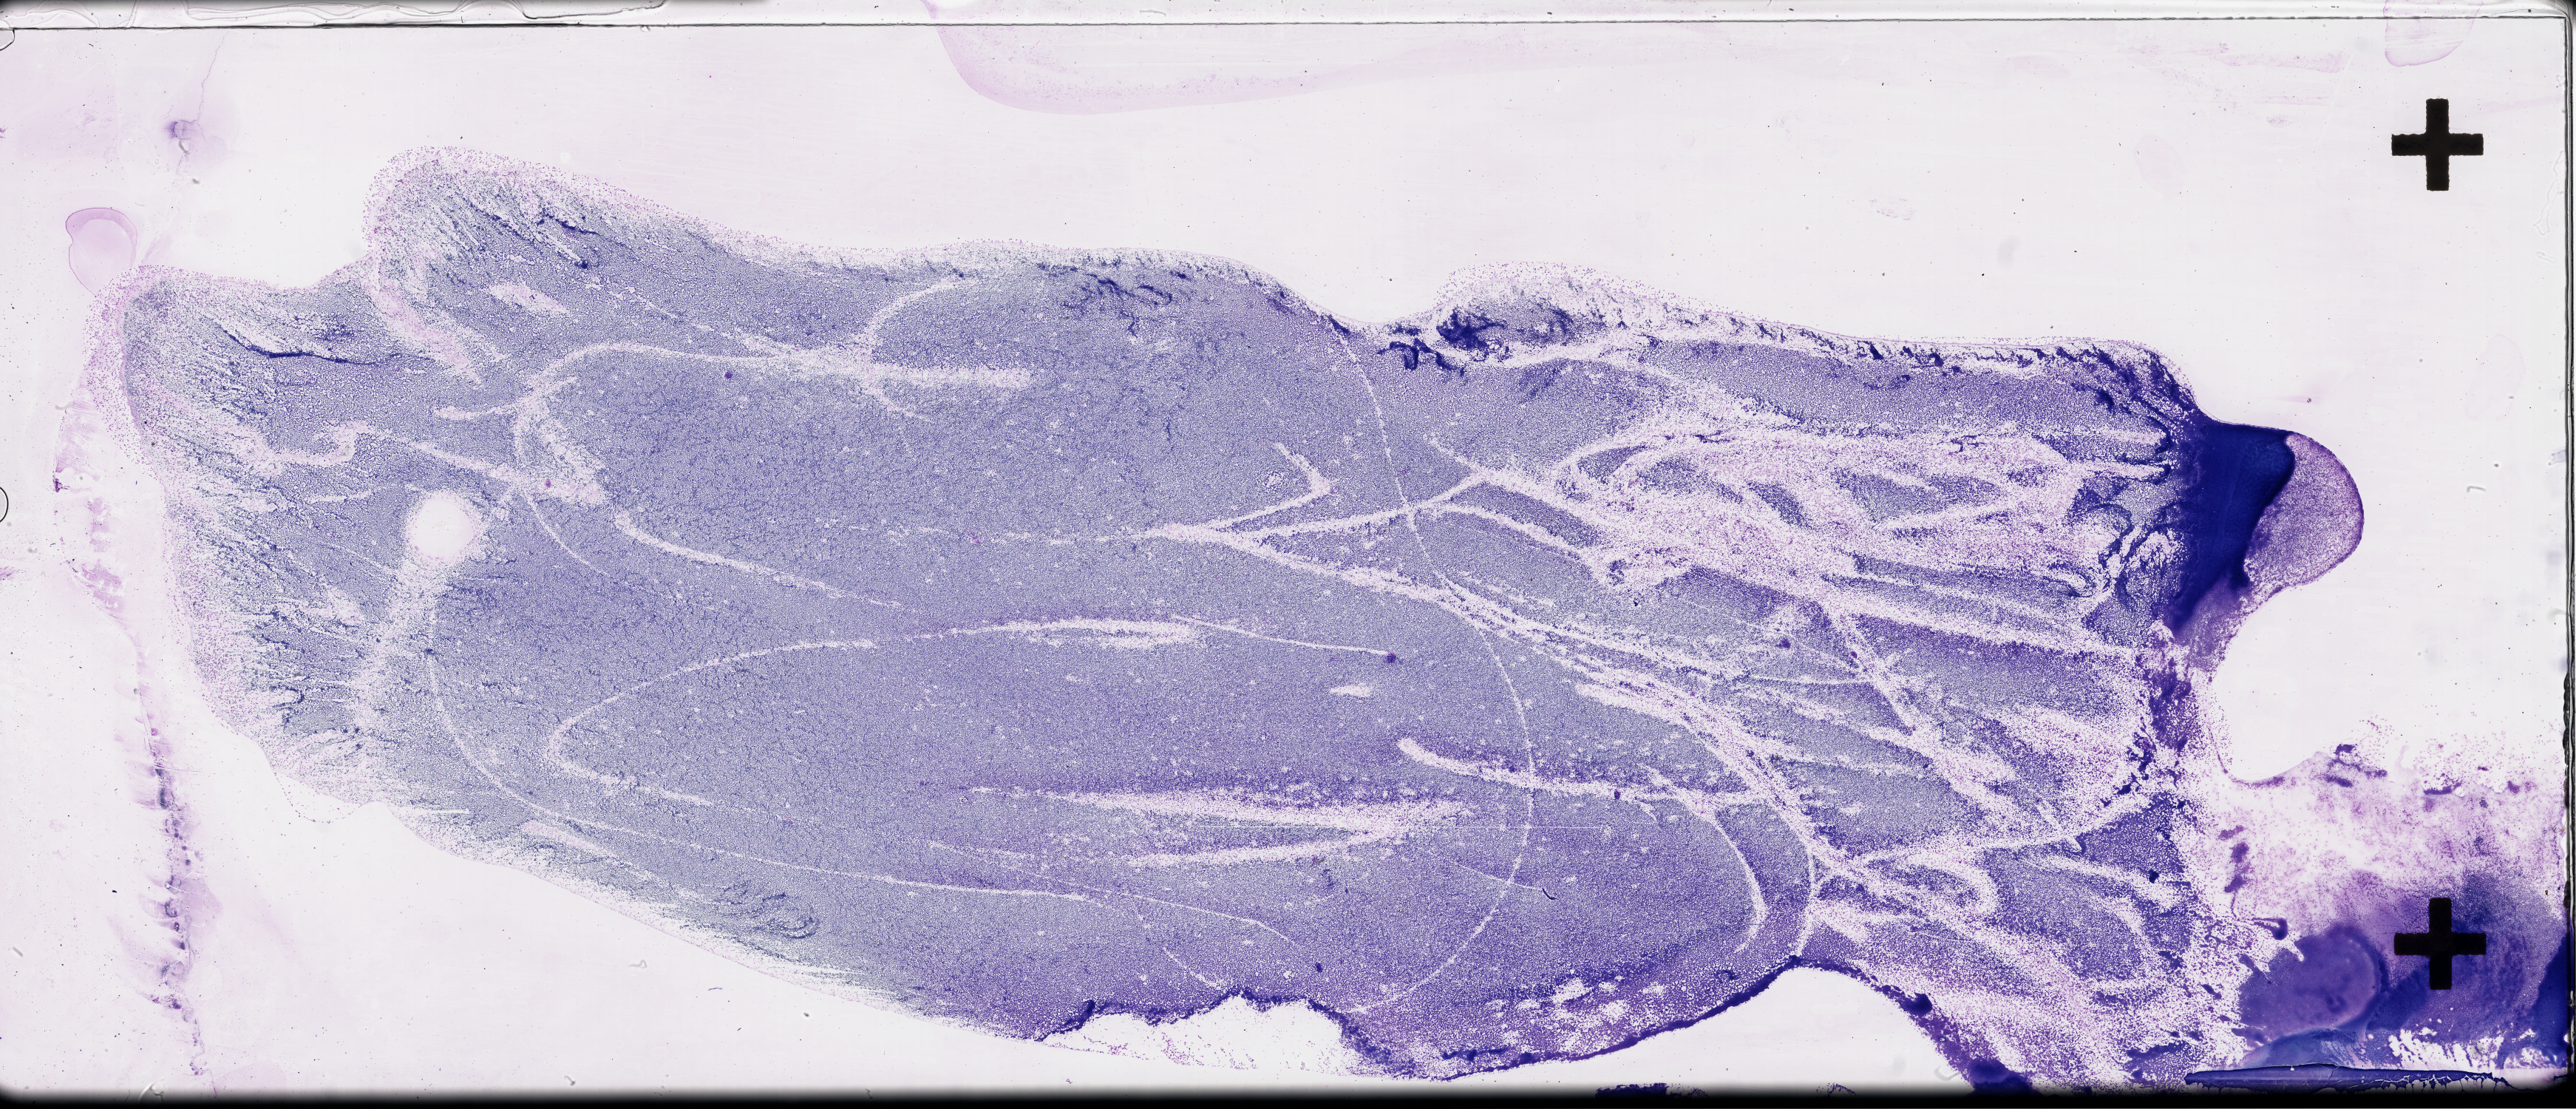
Digitized H&E tissue section (whole slide), whole scanned area (about 56.3 x 24.2 mm) shown as a low-resolution overview, peripheral blood (leukaemic) sample.
FAB classification: M4. Diagnosis: Acute Myeloid Leukemia.